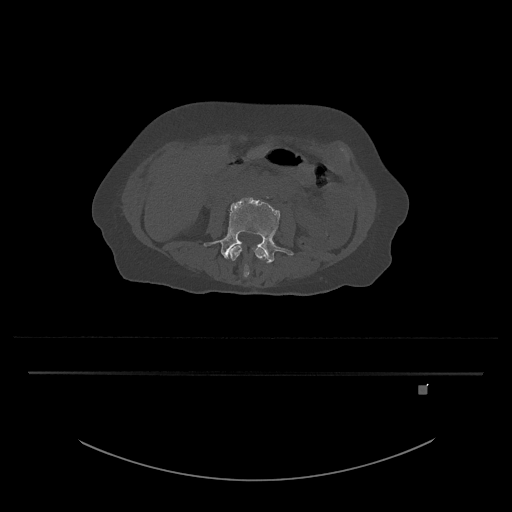
CT including the spine, one axial slice; position 384 of 797 along the scan axis; reconstruction kernel Br40s/3; bone window (W 1800 / L 400 HU); 0.5 mm slice thickness; 512 × 512 image matrix, field of view 500 × 500 mm. Patient: female, 57 years. Case-level facts recorded for this patient, not image findings: primary cancer: cervical.
Annotated regions visible in this slice (semi-automatically segmented with operator editing):
- L3 vertebra: bounding box <229,245,267,278> (left, top, right, bottom; pixels)
- L4 vertebra: <204,197,294,264>